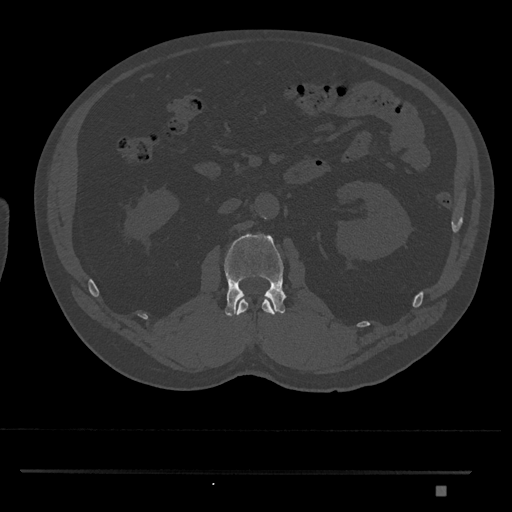
CT including the spine, one axial slice. 120 kVp. Bone window (W 1800 / L 400 HU). 512 × 512 image matrix. Patient: male, 65 years. Case-level facts recorded for this patient, not image findings: primary cancer: prostate.
Annotated regions visible in this slice (semi-automatically segmented with operator editing):
- L1 vertebra: bounding box [x1, y1, x2, y2] px = [237, 298, 275, 316]
- L2 vertebra: [223, 234, 286, 316]